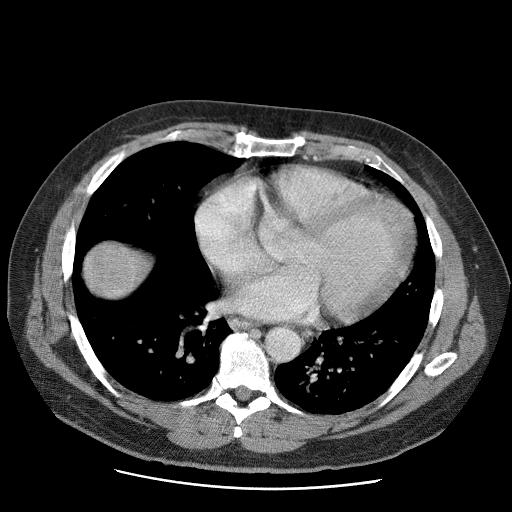
Contrast-enhanced abdominal CT (liver protocol), one axial slice; slice 69 of 81 in the series (ordered by position); reconstruction kernel STANDARD; 120 kVp; soft-tissue window (W 400 / L 40 HU); 2.5 mm slice thickness; 512 × 512 image matrix, field of view 380 × 380 mm. Case-level facts recorded for this patient, not image findings: diagnosis: hepatocellular carcinoma (patient treated with transarterial chemoembolisation; whether this scan precedes or follows treatment is not stated here); TNM stage (as recorded): Stage-IIIA; Child-Pugh class: A; tumour differentiation: moderately differentiated; tumour nodularity: multinodular.
Outlined on this slice (semi-automatic segmentation, software-assisted and operator-edited):
- liver parenchyma outside the tumour (the mass and vessels are separate outlines, so this box may not span the whole liver): bounding box <84,242,148,296> (left, top, right, bottom; pixels)
- mass: <83,241,135,297>